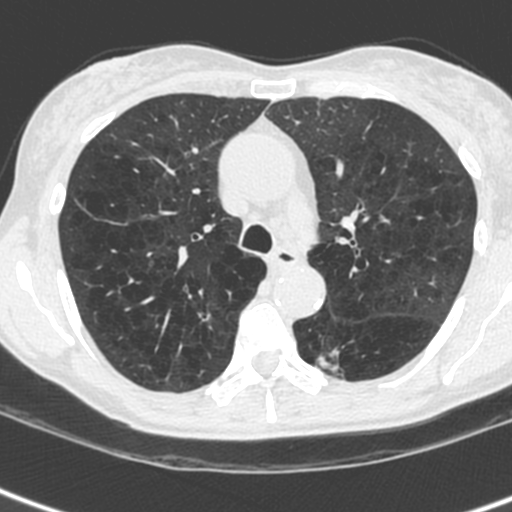
Low-dose screening chest CT, axial slice; baseline annual screen; lung window (W 1500 / L -600 HU); 1.3 mm slice thickness; 120 kVp. Female participant, aged 61 years at enrolment. Current smoker at enrolment.
• Lesion marked by an expert reader, box from (x=182, y=300) to (x=225, y=338) px.
• No non-calcified nodule or mass ≥4 mm was recorded by the screening reader at this exam.